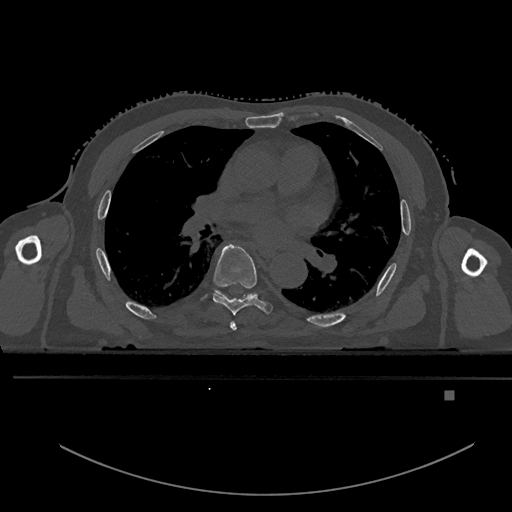
CT including the spine, one axial slice. Position 303 of 969 along the scan axis. Bone window (W 1800 / L 400 HU). 512 × 512 image matrix, field of view 456 × 456 mm. Patient: male, 82 years. From the clinical record (not read from this slice): primary cancer: prostate.
Outlined on this slice (semi-automatic segmentation, software-assisted and operator-edited):
- T5 vertebra: bounding box <230,322,237,331> (left, top, right, bottom; pixels)
- T6 vertebra: <212,244,273,315>
- T7 vertebra: <249,294,253,297>